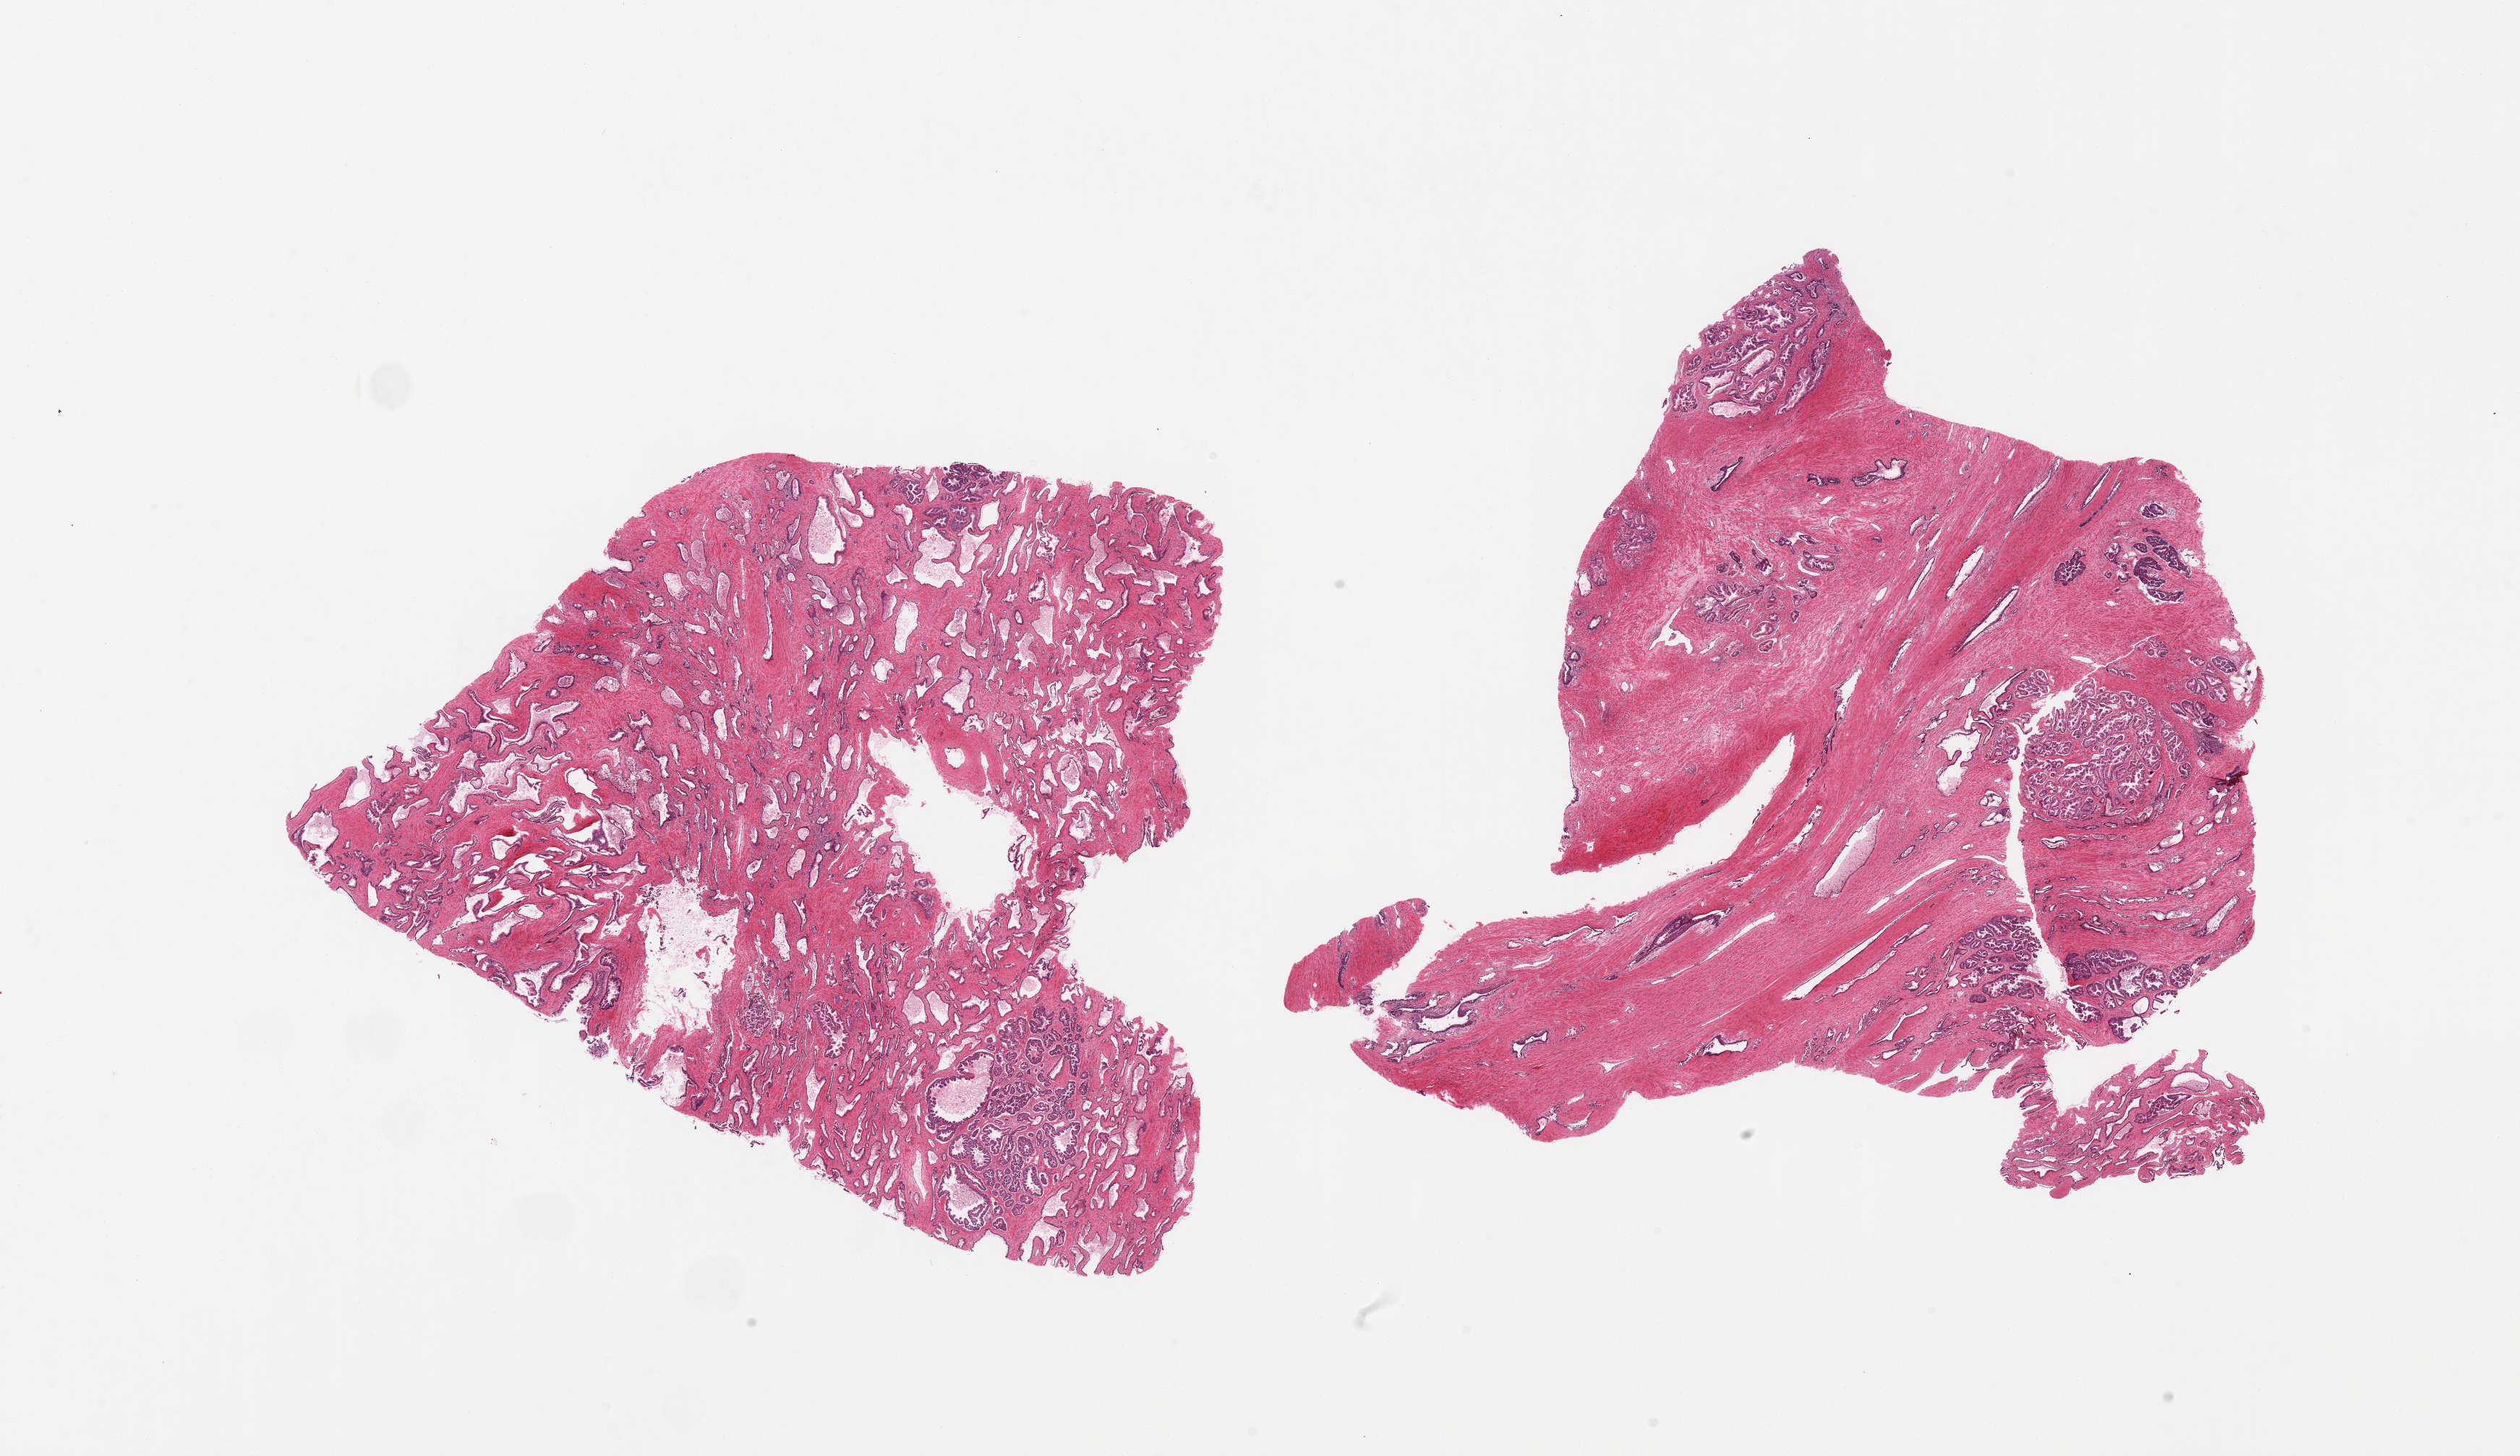
Whole-slide image, H&E stain, brightfield, shown as a low-resolution overview of the whole scanned area (about 27.6 x 15.9 mm, slide scanned at 20x). PAXgene-fixed paraffin-embedded (PFPE) section. Section of prostate (target tissue). Donor tissue sample. Male donor.
Reviewer comment on this tissue sample: 2 pieces, glandular hyperplastic pattern.